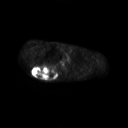
FDG PET of an extremity soft-tissue mass (from a PET/CT study), one axial slice. Slice 192 of 267 in the series (ordered by position). 128 × 128 image matrix, field of view 700 × 700 mm. Male patient, age 61 years. From the clinical record (not read from this slice): histological type: pleiomorphic spindle cell undifferentiated; grade: high; site of the primary tumour: right parascapusular.
Structures marked on this image (expert contour drawn on MRI and transferred to this co-registered scan by the dataset authors):
- gross tumour volume including surrounding oedema: bounding box (x1, y1, x2, y2) in pixels: (32, 64, 60, 79)
- gross tumour volume (mass): (32, 64, 56, 78)